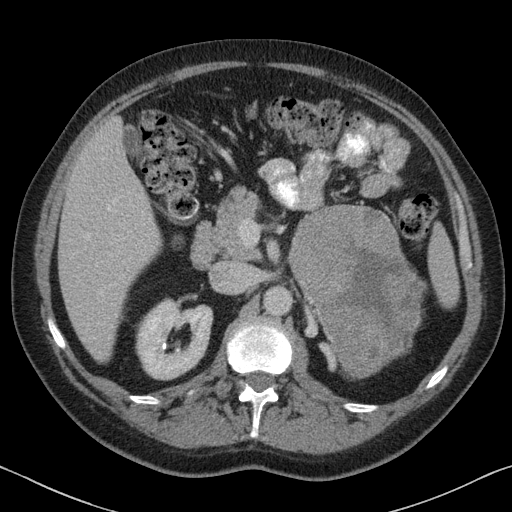
Contrast-enhanced abdominal CT, one axial slice. Position 44 of 88 along the scan axis. Reconstruction kernel B31f. 120 kVp. Soft-tissue window (W 400 / L 40 HU). 3 mm slice thickness. 512 × 512 image matrix, field of view 366 × 366 mm. Male patient, age 51 years. From the clinical record (not read from this slice): diagnosis: adrenocortical carcinoma; tumour side: left adrenal; tumour size at pathology: 16.5 cm; Ki-67 index: 30 %.
Outlined on this slice (semi-automatically segmented with operator editing):
- mass: bounding box [x1, y1, x2, y2] px = [290, 206, 422, 379]